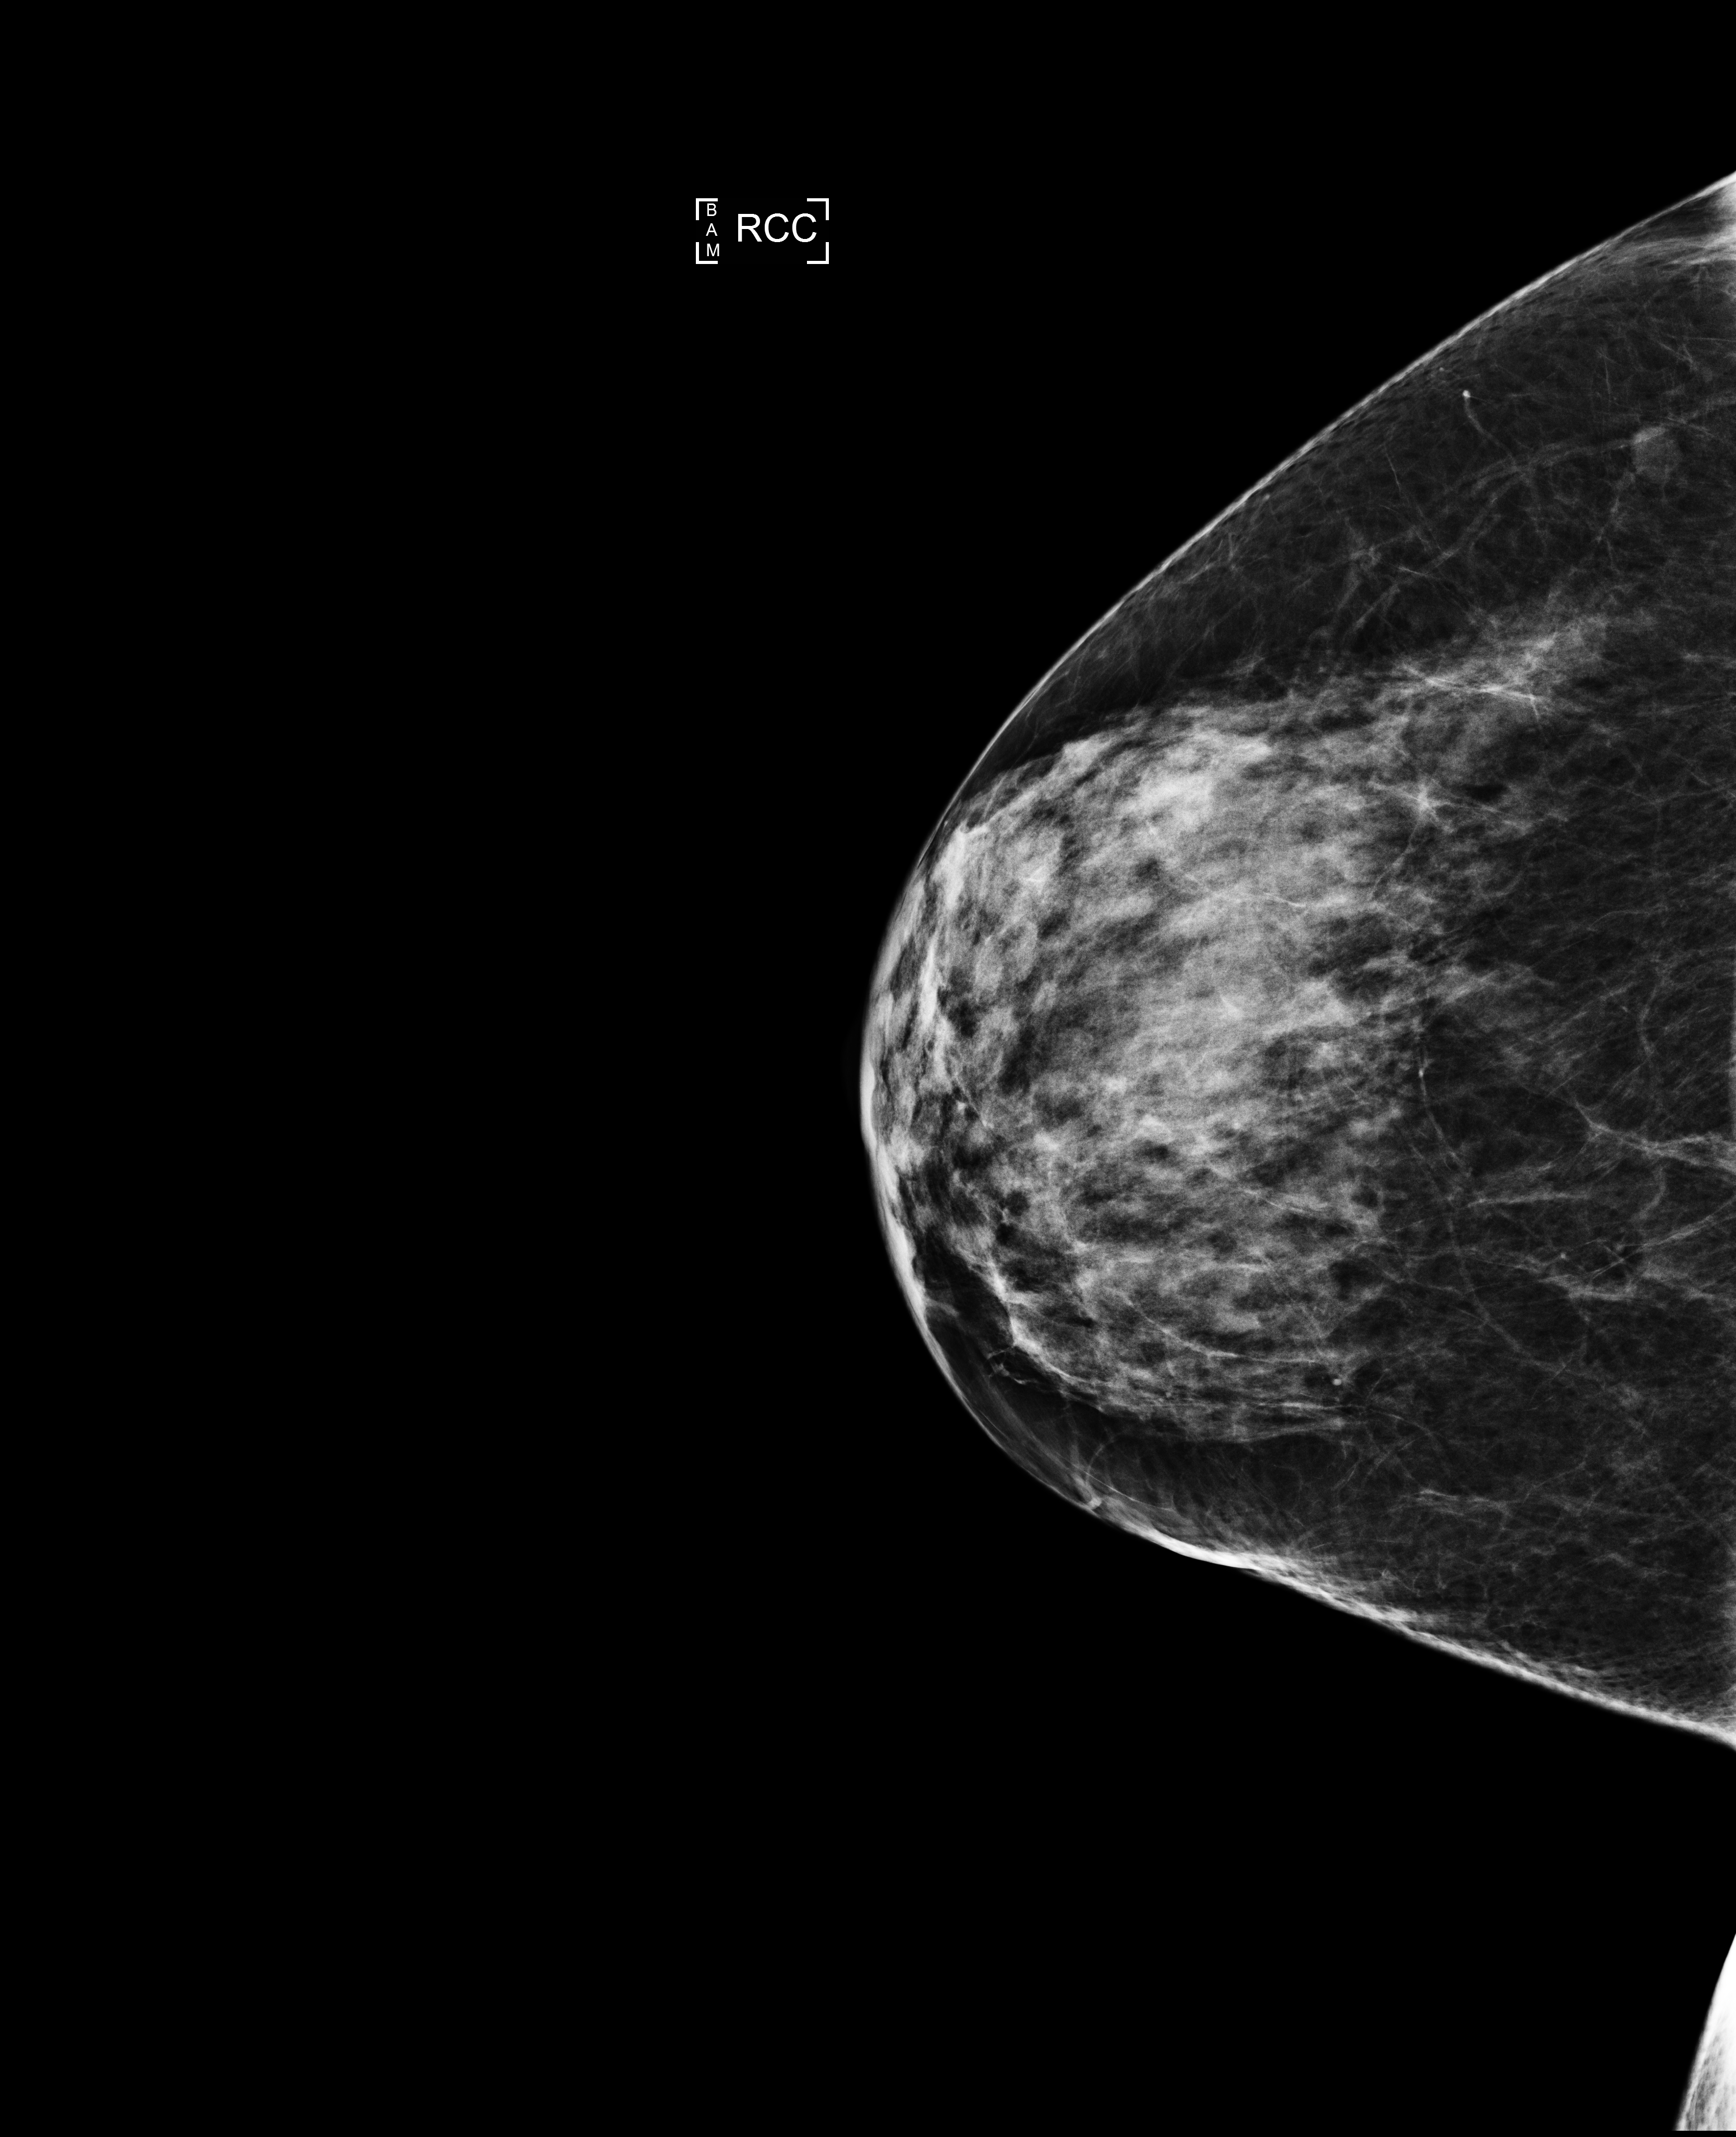
Annual screening mammography examination. Patient aged 55 years (female).
Image type: full-field digital mammogram. Breast: right. Projection: CC view.